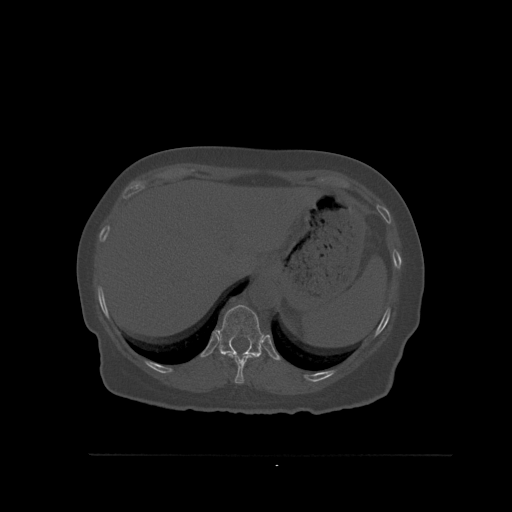
CT including the spine, one axial slice; slice 308 of 527 in the series (ordered by position); bone window (W 1800 / L 400 HU); 1.5 mm slice thickness; 512 × 512 image matrix, field of view 470 × 470 mm. Female patient, age 73 years. Case-level facts recorded for this patient, not image findings: primary cancer: breast.
Structures marked on this image (semi-automatically segmented with operator editing):
- T10 vertebra: bounding box [x1, y1, x2, y2] px = [226, 353, 257, 384]
- T11 vertebra: [218, 304, 265, 359]